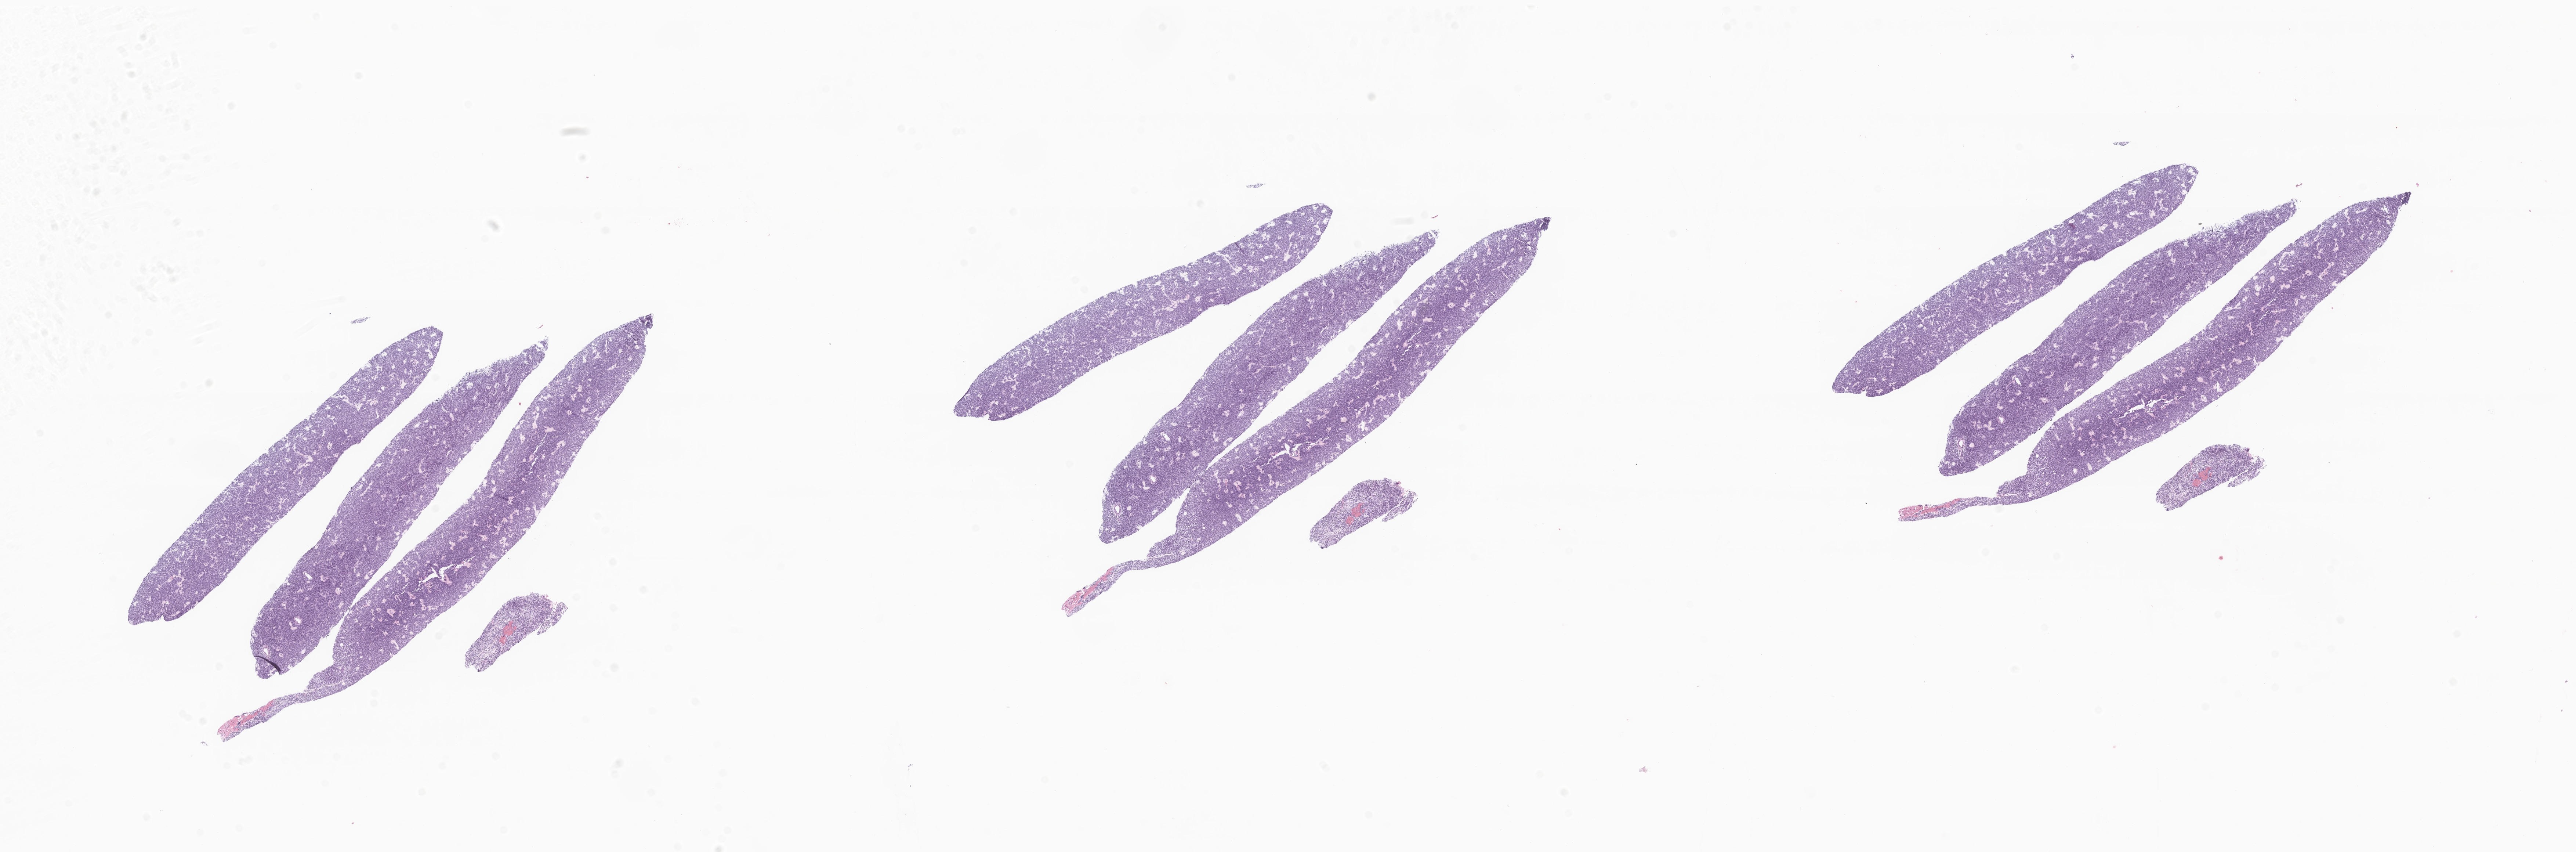
Whole-slide image, hematoxylin and eosin (H&E) stain of tumor tissue from the long bone of upper limb — whole scanned area (about 29.6 x 9.8 mm) shown as a low-resolution overview, formalin-fixed, paraffin-embedded (FFPE) tissue. Female patient, age 108 months (9 years).
Diagnosis (ICD-O-3 morphology term): Sarcoma, NOS.